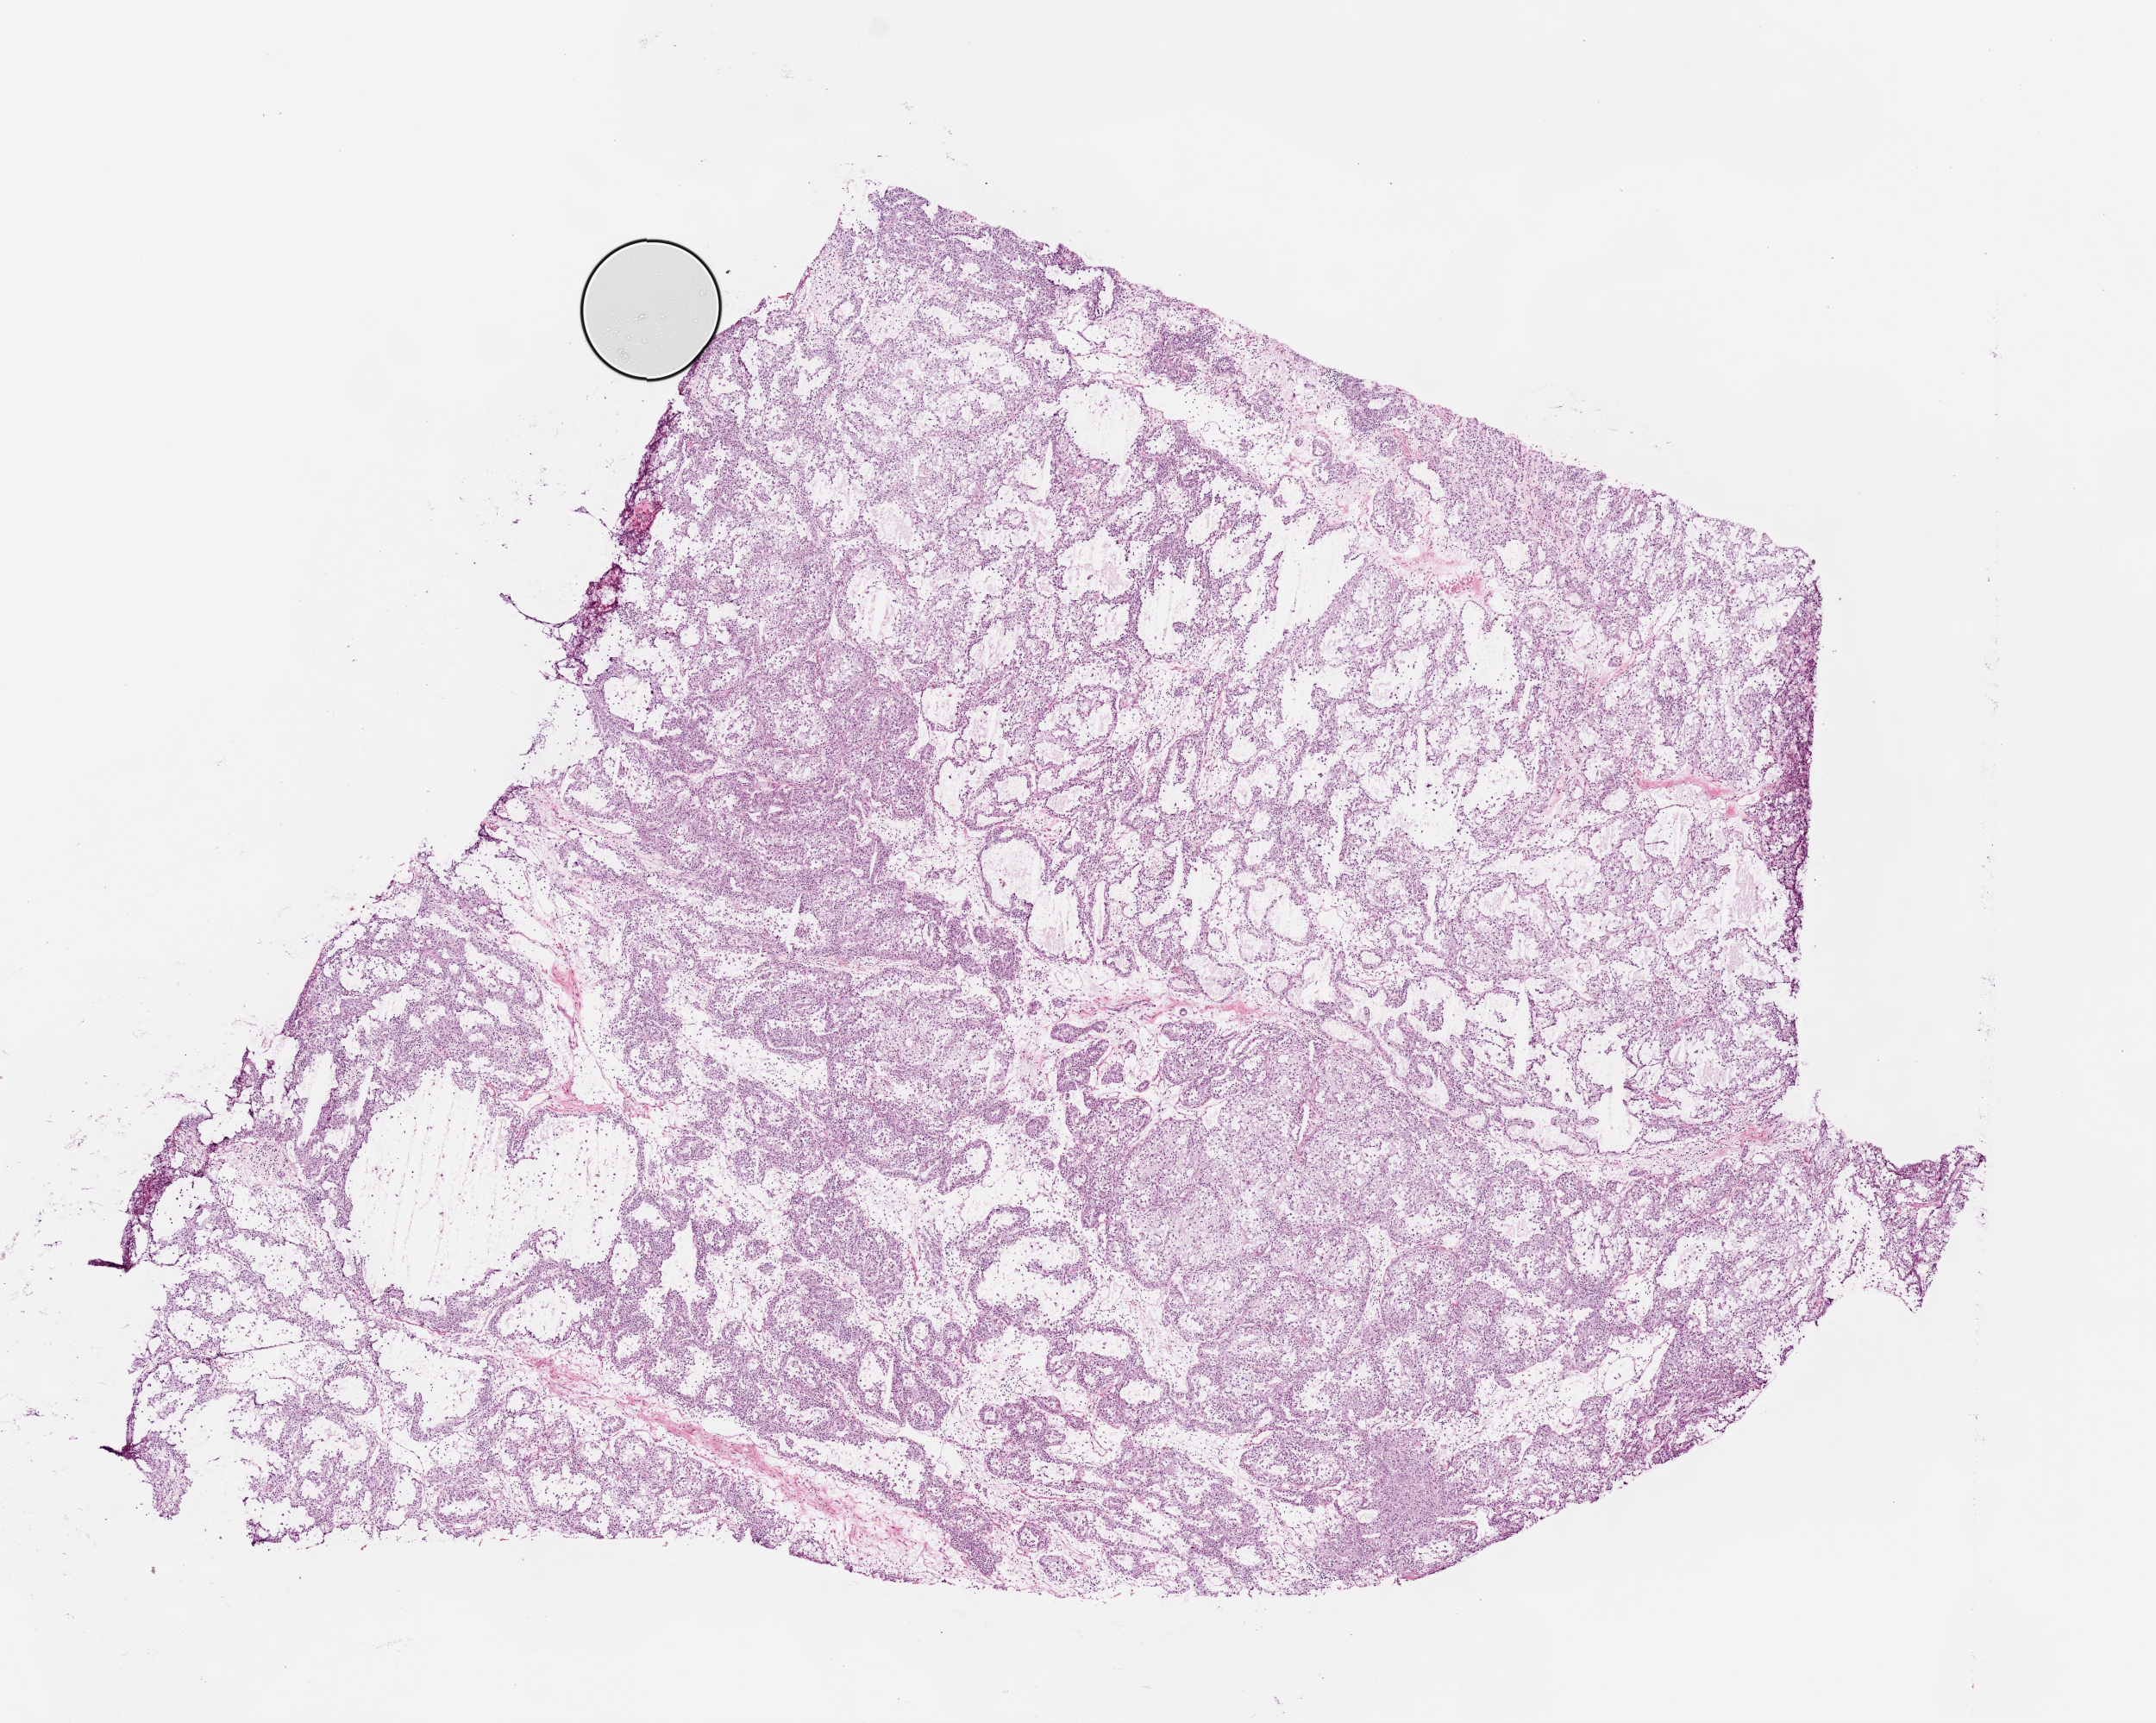
Digitized H&E-stained tissue section (whole slide) — low-resolution overview of the scanned area, about 10.0 x 8.0 mm, frozen section from the bottom of the tissue portion, sample: primary tumour, kidney. Male, age 65 years at initial diagnosis.
Pathologic diagnosis: Clear cell adenocarcinoma, NOS.